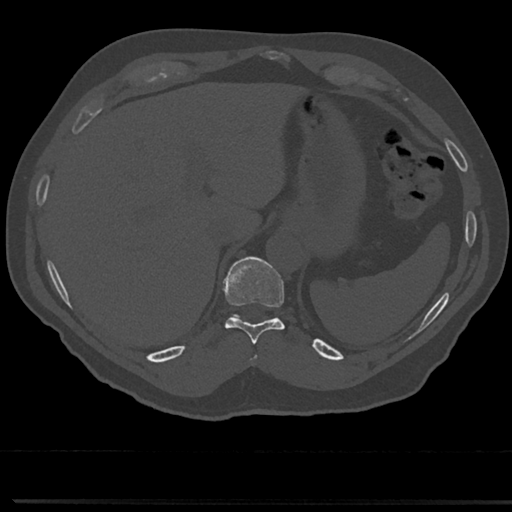
CT including the spine, one axial slice. Position 249 of 817 along the scan axis. Bone window (W 1800 / L 400 HU). 0.5 mm slice thickness. 512 × 512 image matrix, field of view 355 × 355 mm. Patient: male, 61 years. Case-level facts recorded for this patient, not image findings: primary cancer: prostate.
Structures marked on this image (semi-automatic segmentation, software-assisted and operator-edited):
- T10 vertebra: bounding box (x1, y1, x2, y2) in pixels: (214, 258, 294, 343)
- T9 vertebra: (250, 351, 259, 368)